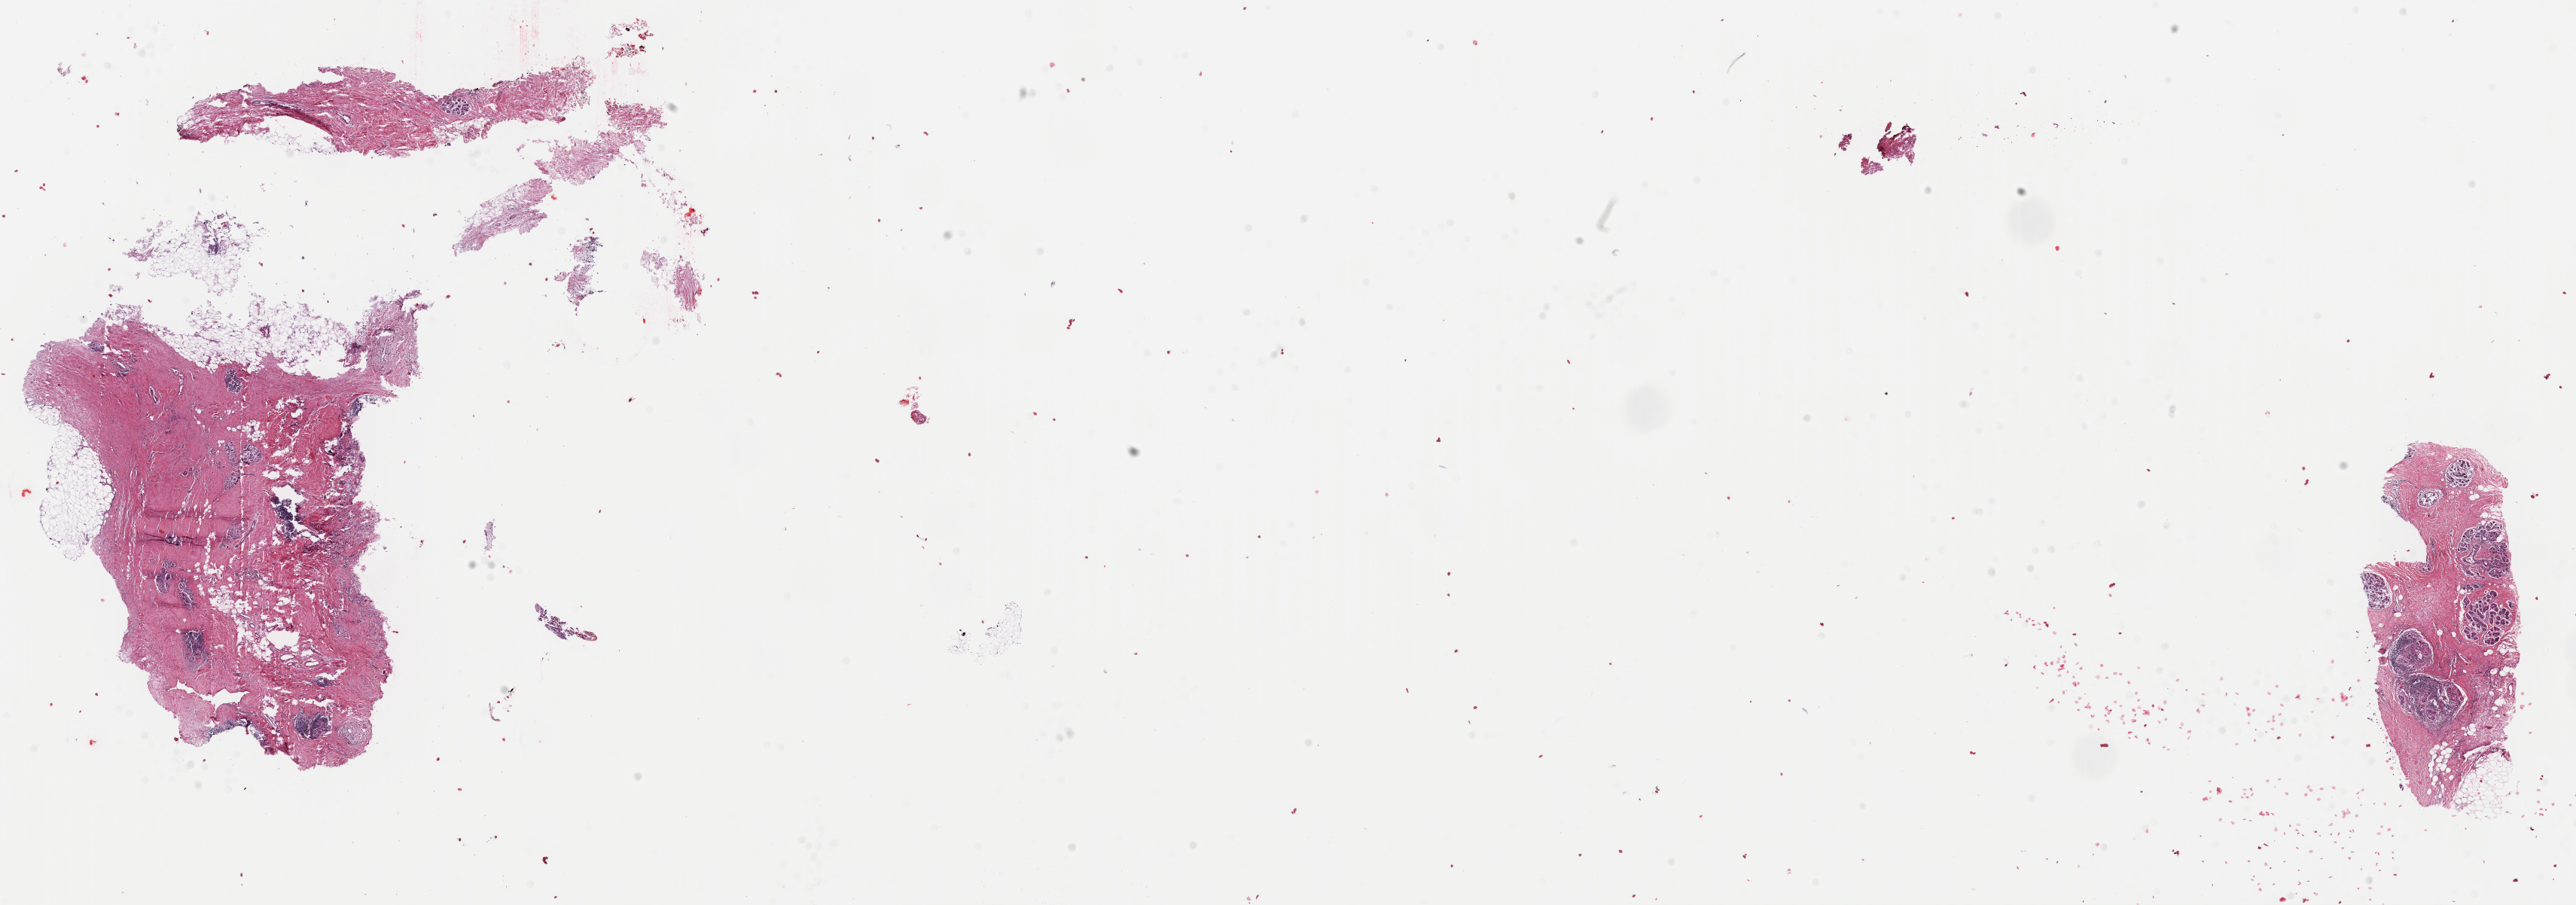
Whole-slide histology image, H&E-stained, shown as a low-resolution overview of the whole scanned area (about 27.0 x 9.5 mm, acquisition: 40x scan). FFPE section. Sample: primary tumour, breast. Female, age 47 years at initial diagnosis.
- TNM: T1 N1 M0
- AJCC pathologic stage: IIA (6th edition)
- lymph nodes positive (case pathology): 2 of 39 examined
- diagnosis: Infiltrating duct carcinoma, NOS